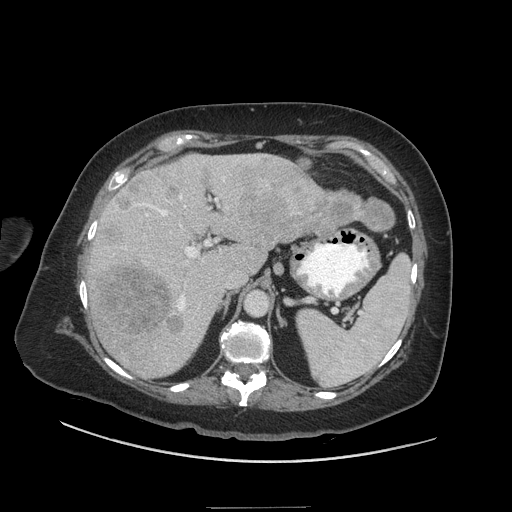
Contrast-enhanced abdominal CT (liver protocol), one axial slice. Slice 32 of 81 in the series (ordered by position). Reconstruction kernel STANDARD. 140 kVp. Soft-tissue window (W 400 / L 40 HU). 512 × 512 image matrix. From the clinical record (not read from this slice): diagnosis: hepatocellular carcinoma (patient treated with transarterial chemoembolisation; whether this scan precedes or follows treatment is not stated here); TNM stage (as recorded): Stage-II; Child-Pugh class: A; tumour differentiation: moderately differentiated; tumour size: 1.7 cm.
Structures marked on this image (semi-automatically segmented with operator editing):
- liver parenchyma outside the tumour (the mass and vessels are separate outlines, so this box may not span the whole liver): box from (x=88, y=154) to (x=318, y=378) px
- mass: (x=89, y=158)–(x=395, y=340)
- liver vessels: (x=110, y=156)–(x=259, y=334)